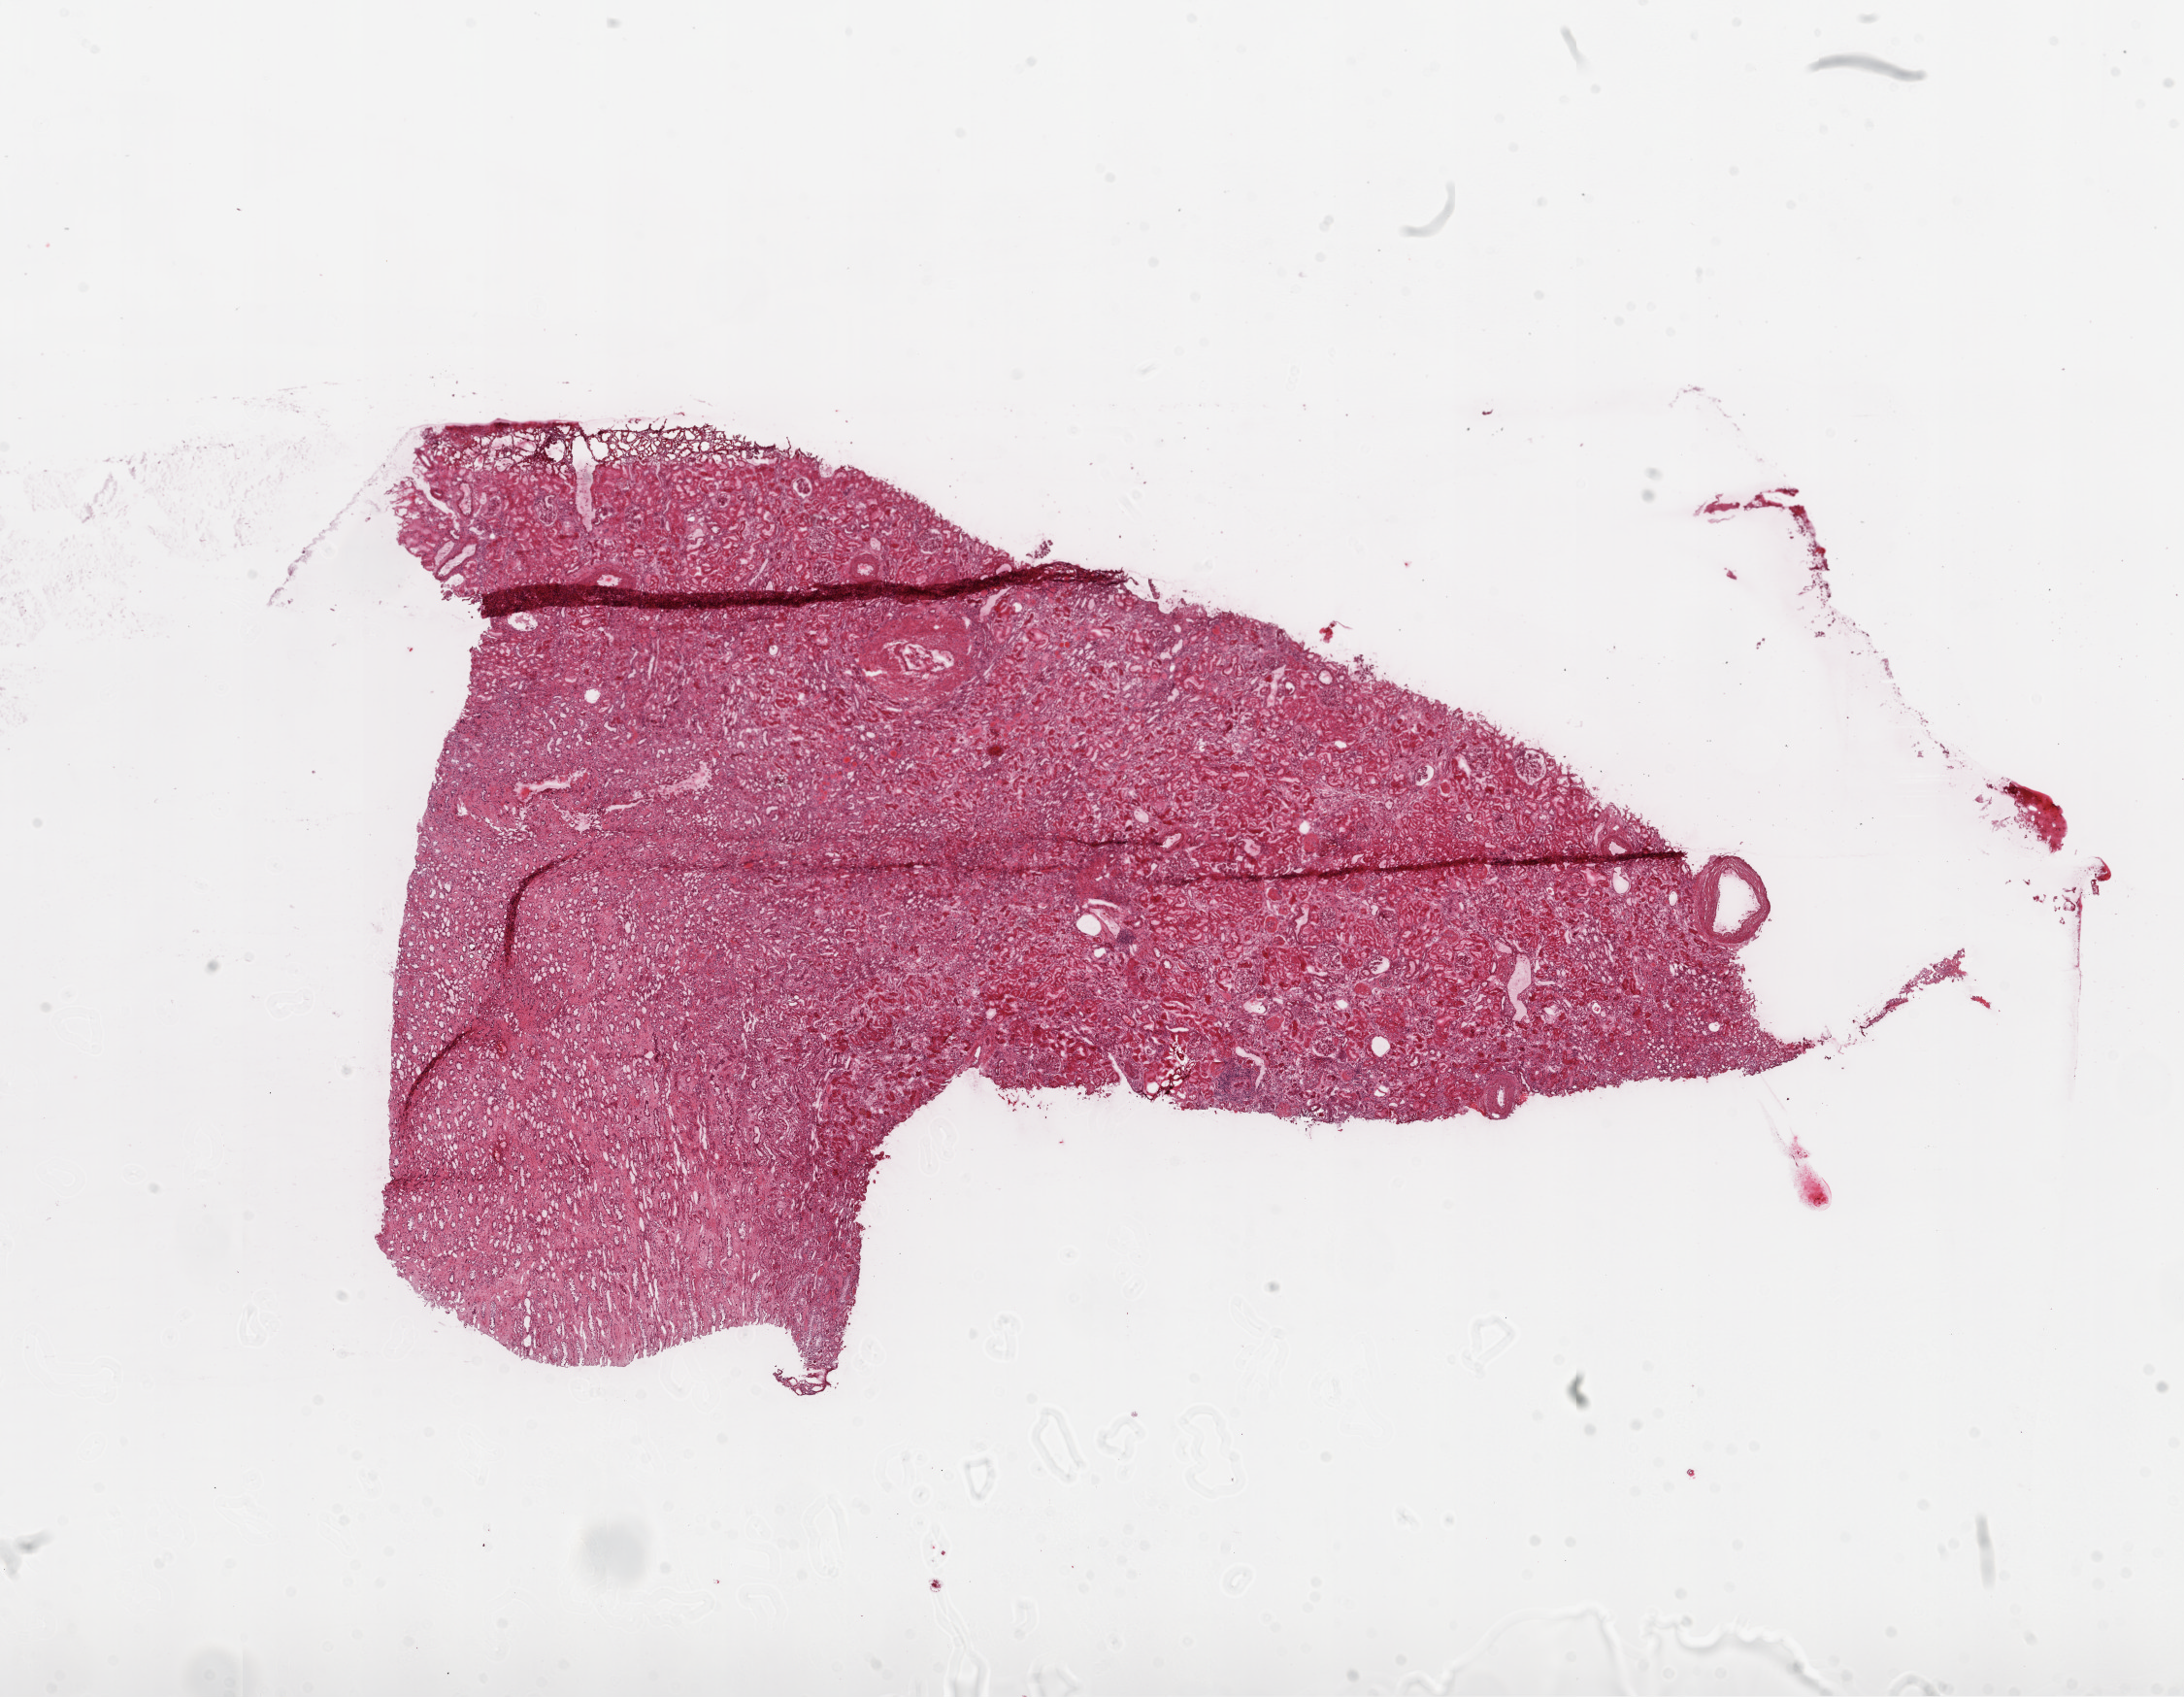
Whole-slide histology image, Hematoxylin and eosin (H&E) stained — shown as a low-resolution overview of the whole scanned area (about 18.1 x 14.0 mm, from a 20x scan); frozen section; sample: solid tissue normal (non-tumour tissue), kidney. Female, age 74 years at initial diagnosis.
This section: solid tissue normal sample (biorepository sample class). Patient diagnosis: Clear cell adenocarcinoma, NOS.